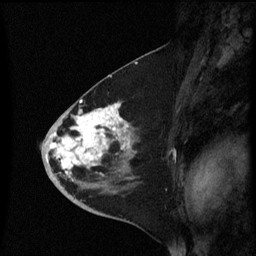
Breast MRI (dynamic contrast-enhanced), one sagittal slice. Slice 32 of 60 in the series (ordered by position). Dynamic contrast-enhanced series, image 2 of 3 at this slice position (ordered by acquisition). 1.5 T. TE 4.2 ms, TR 8.4 ms. 256 × 256 image matrix, field of view 200 × 200 mm. Female patient, age 46 years. From the clinical record (not read from this slice): setting: breast cancer imaged before/during neoadjuvant chemotherapy; receptor status: HER2-positive.
Outlined on this slice (semi-automatic segmentation, software-assisted and operator-edited):
- analysis volume of interest (the breast-tissue region the enhancement analysis was run in; not a lesion): bounding box [x1, y1, x2, y2] px = [42, 96, 137, 187]
- tumour enhancement mask (voxels above the 70 % enhancement threshold inside the analysis volume of interest): [51, 100, 130, 177]